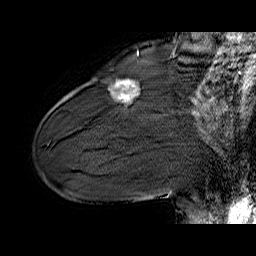
Breast MRI (dynamic contrast-enhanced), one sagittal slice; slice 18 of 60 in the series (ordered by position); dynamic contrast-enhanced series, time point 2 of 6 at this slice position (early post-contrast); 1.5 T; TE 6.4 ms, TR 32.9 ms; 256 × 256 image matrix, field of view 200 × 200 mm. Female patient. Case-level facts recorded for this patient, not image findings: setting: breast cancer imaged before/during neoadjuvant chemotherapy; receptor status: HER2-positive.
Annotated regions visible in this slice (semi-automatically segmented with operator editing):
- analysis volume of interest (the breast-tissue region the enhancement analysis was run in; not a lesion): bounding box <110,80,139,104> (left, top, right, bottom; pixels)
- tumour enhancement mask (voxels above the 100 % enhancement threshold inside the analysis volume of interest): <127,80,130,82>